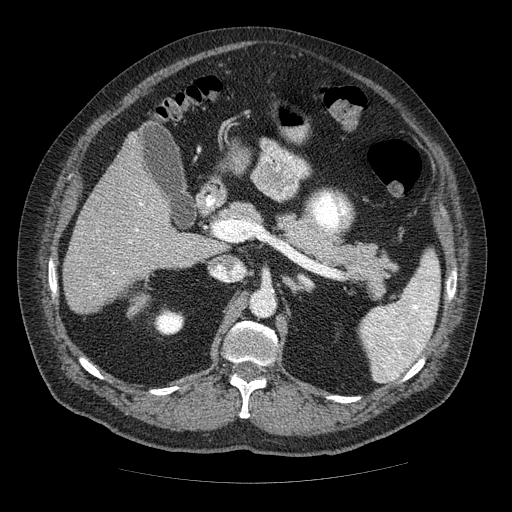
Contrast-enhanced abdominal CT (liver protocol), one axial slice; position 26 of 85 along the scan axis; reconstruction kernel STANDARD; soft-tissue window (W 400 / L 40 HU); 512 × 512 image matrix, field of view 420 × 420 mm. Case-level facts recorded for this patient, not image findings: diagnosis: hepatocellular carcinoma (patient treated with transarterial chemoembolisation; whether this scan precedes or follows treatment is not stated here); TNM stage (as recorded): Stage-IIIA; Child-Pugh class: A; tumour size: 7 cm.
Annotated regions visible in this slice (semi-automatically segmented with operator editing):
- liver parenchyma outside the tumour (the mass and vessels are separate outlines, so this box may not span the whole liver): bounding box <62,132,216,312> (left, top, right, bottom; pixels)
- liver vessels: <112,203,158,274>